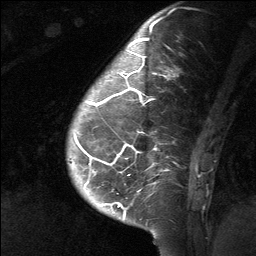
Breast MRI (dynamic contrast-enhanced), one sagittal slice; position 17 of 64 along the scan axis; dynamic contrast-enhanced study with each time point stored as its own series, time point 2 of 3 at this slice position (early post-contrast, ordered by acquisition time); 1.5 T; TE 4.8 ms, TR 27 ms; 2 mm slice thickness; 256 × 256 image matrix, field of view 180 × 180 mm. Patient: female, 39 years. Case-level facts recorded for this patient, not image findings: setting: breast cancer imaged before/during neoadjuvant chemotherapy; receptor status: HER2-positive.
Structures marked on this image (semi-automatic segmentation, software-assisted and operator-edited):
- analysis volume of interest (the breast-tissue region the enhancement analysis was run in; not a lesion): box from (x=66, y=40) to (x=201, y=217) px
- tumour enhancement mask (voxels above the 90 % enhancement threshold inside the analysis volume of interest): (x=75, y=40)–(x=168, y=217)